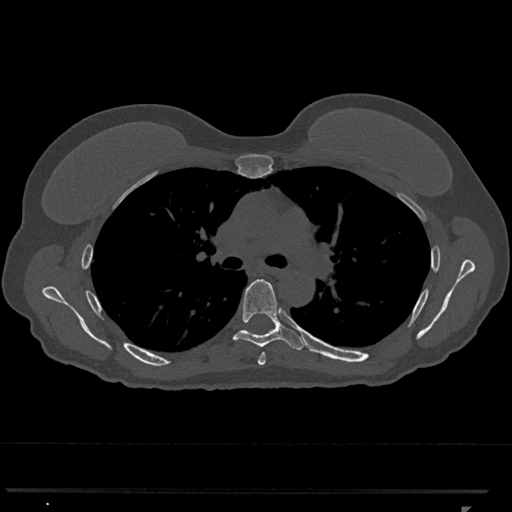
CT including the spine, one axial slice. Slice 766 of 793 in the series (ordered by position). 120 kVp. Bone window (W 1800 / L 400 HU). 0.5 mm slice thickness. 512 × 512 image matrix, field of view 380 × 380 mm. Patient: female, 62 years. From the clinical record (not read from this slice): primary cancer: renal.
Structures marked on this image (semi-automatic segmentation, software-assisted and operator-edited):
- T5 vertebra: bounding box (x1, y1, x2, y2) in pixels: (258, 353, 266, 365)
- T6 vertebra: (222, 279, 305, 350)